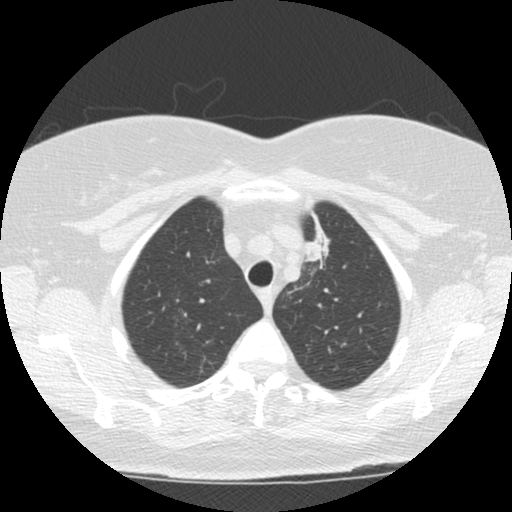
Low-dose screening chest CT, one axial slice. Position 97 of 120 along the scan axis. Reconstruction kernel STANDARD. 120 kVp. Lung window (W 1500 / L -600 HU). 512 × 512 image matrix.
Annotated regions visible in this slice (expert manual segmentation):
- lesion 1 (tumor, upper lobe of left lung): bounding box (x1, y1, x2, y2) in pixels: (305, 212, 330, 262)